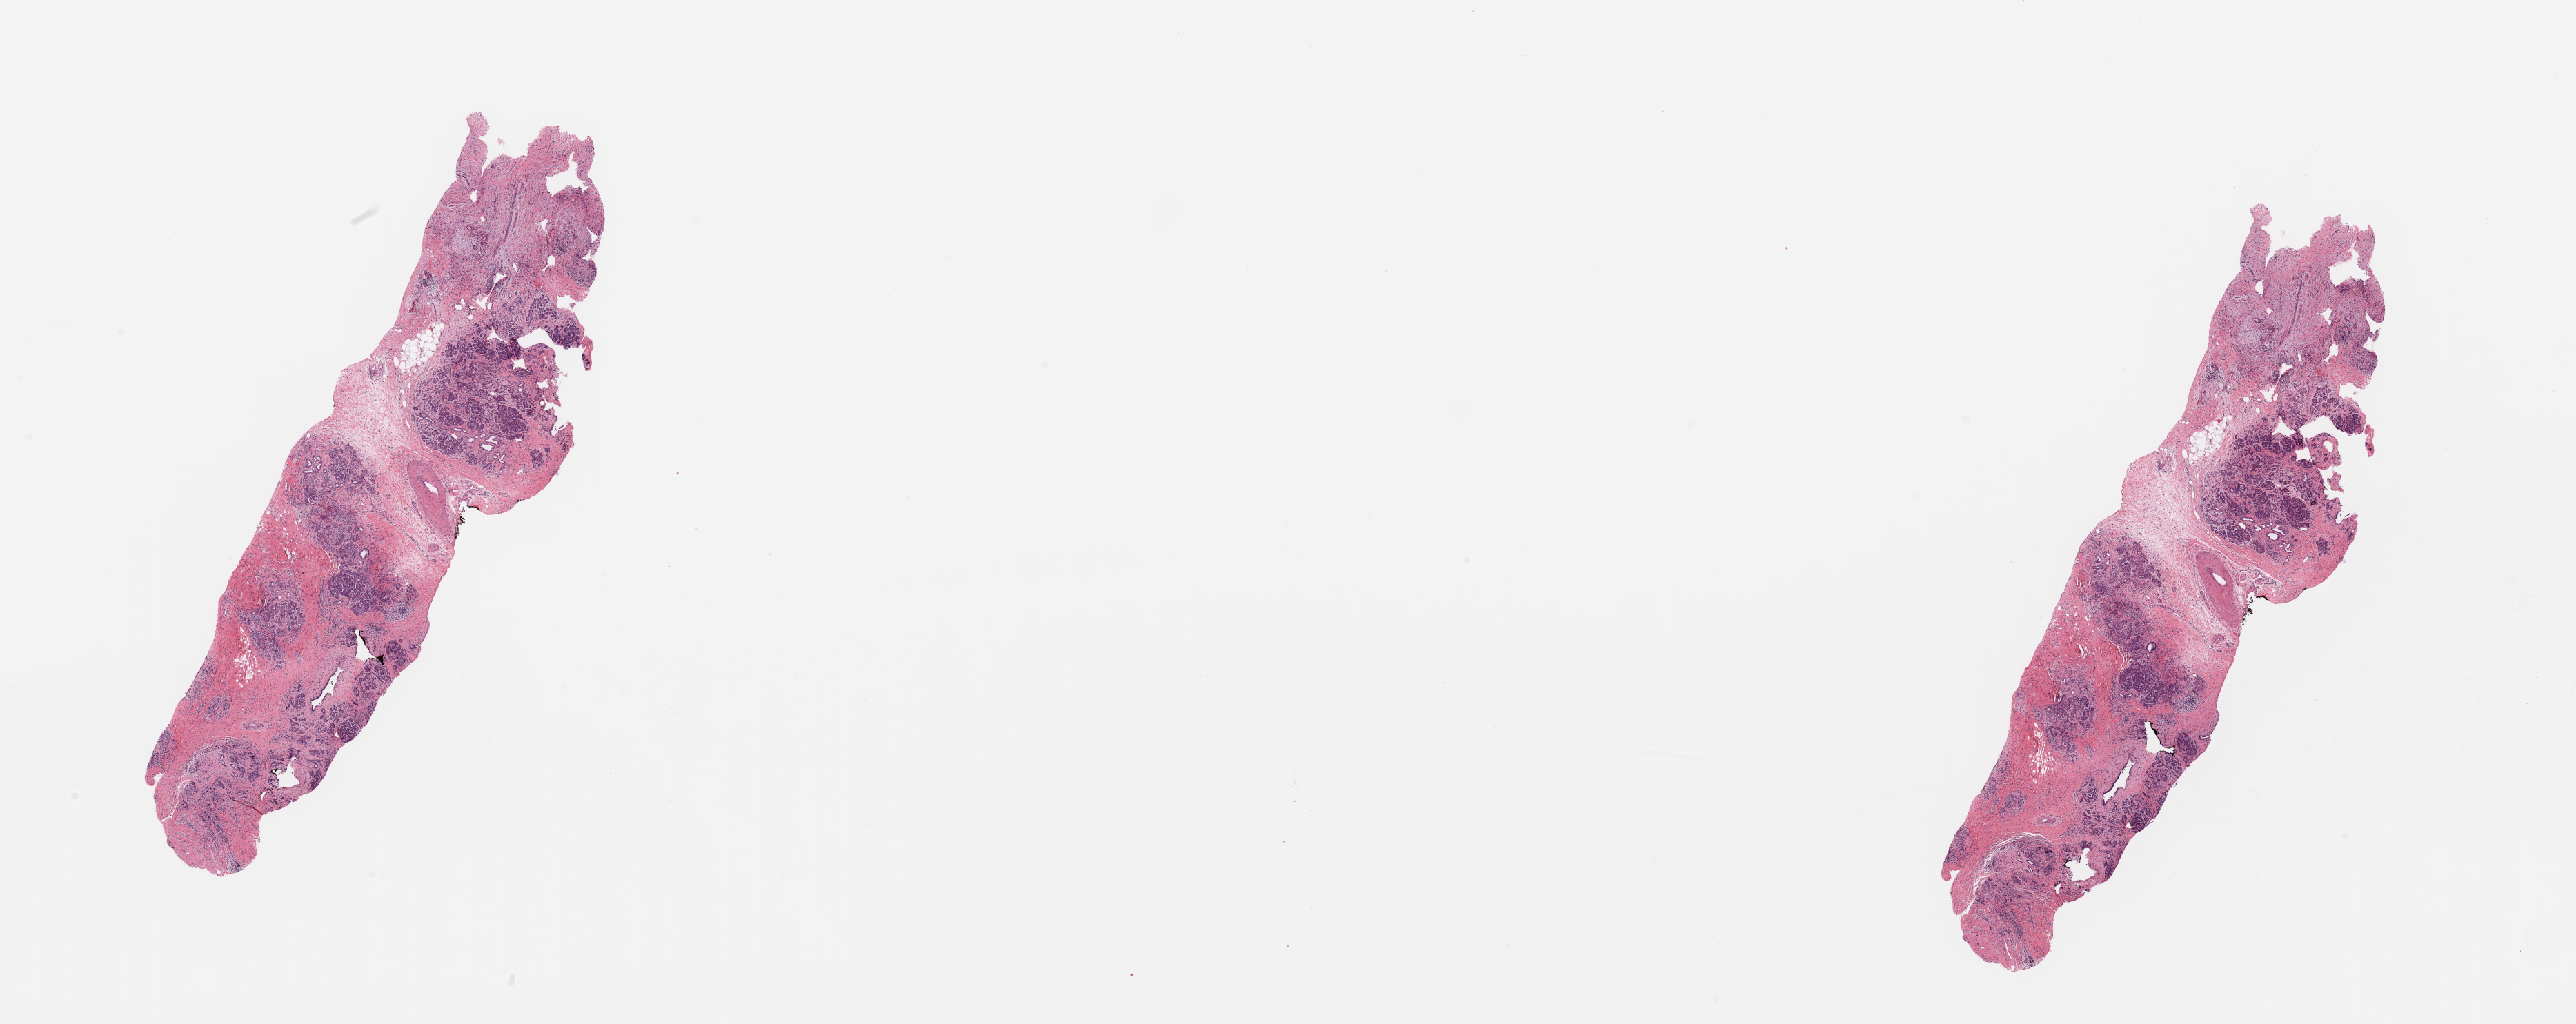
Whole-slide histology image, H&E-stained — a low-resolution overview of the entire scanned area, about 29.5 x 11.7 mm, tumour tissue sample, sampled site: pancreas. Patient: male, age 80 years. Histologic grade: G2 (moderately differentiated). Composition of this section per pathologist review: tumour nuclei 5%, necrosis 0%.
* primary tumour site (as recorded): head
* AJCC pathologic stage: IIB
* diagnosis: Infiltrating duct carcinoma, NOS